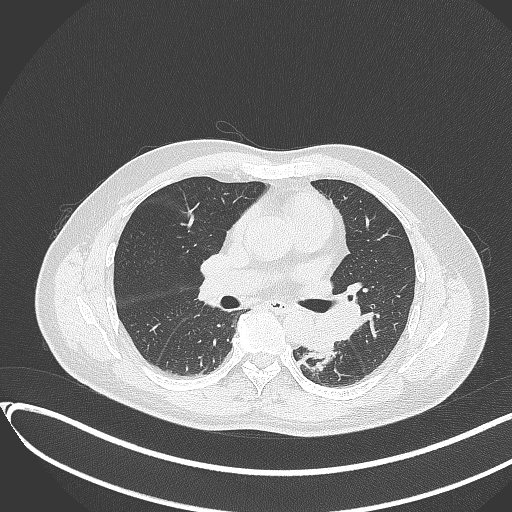
Chest CT, one axial slice; position 189 of 417 along the scan axis; 120 kVp; lung window (W 1500 / L -600 HU); 1 mm slice thickness; 512 × 512 image matrix, field of view 400 × 400 mm. Patient: male, 54 years. Case-level facts recorded for this patient, not image findings: clinical TNM (as recorded): T3 N0 M0.
Annotated regions visible in this slice (rectangle marked by the reading radiologist):
- lung tumour (recorded histology: squamous cell carcinoma): bounding box <301,316,337,353> (left, top, right, bottom; pixels)